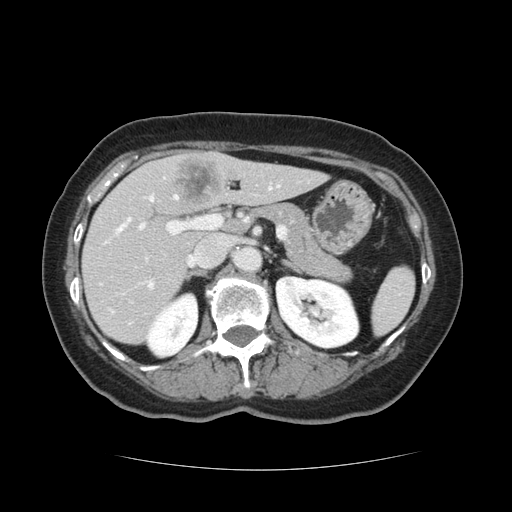
Contrast-enhanced abdominal CT, one axial slice. Slice 68 of 128 in the series (ordered by position). 120 kVp. Intravenous contrast given. Soft-tissue window (W 400 / L 40 HU). 2.5 mm slice thickness. 512 × 512 image matrix. Female patient, age 67 years. Case-level facts recorded for this patient, not image findings: diagnosis: colorectal cancer liver metastases, imaged before liver resection; multiple liver metastases: yes; largest metastasis: 3 cm; disease in both lobes: yes.
Annotated regions visible in this slice (expert manual segmentation):
- hepatic veins: bounding box [x1, y1, x2, y2] px = [118, 186, 280, 262]
- liver: [83, 152, 323, 344]
- planned liver remnant (the part of the liver to remain after resection): [83, 162, 323, 344]
- portal vein (with intrahepatic branches): [139, 182, 272, 290]
- liver metastasis: [173, 159, 220, 206]